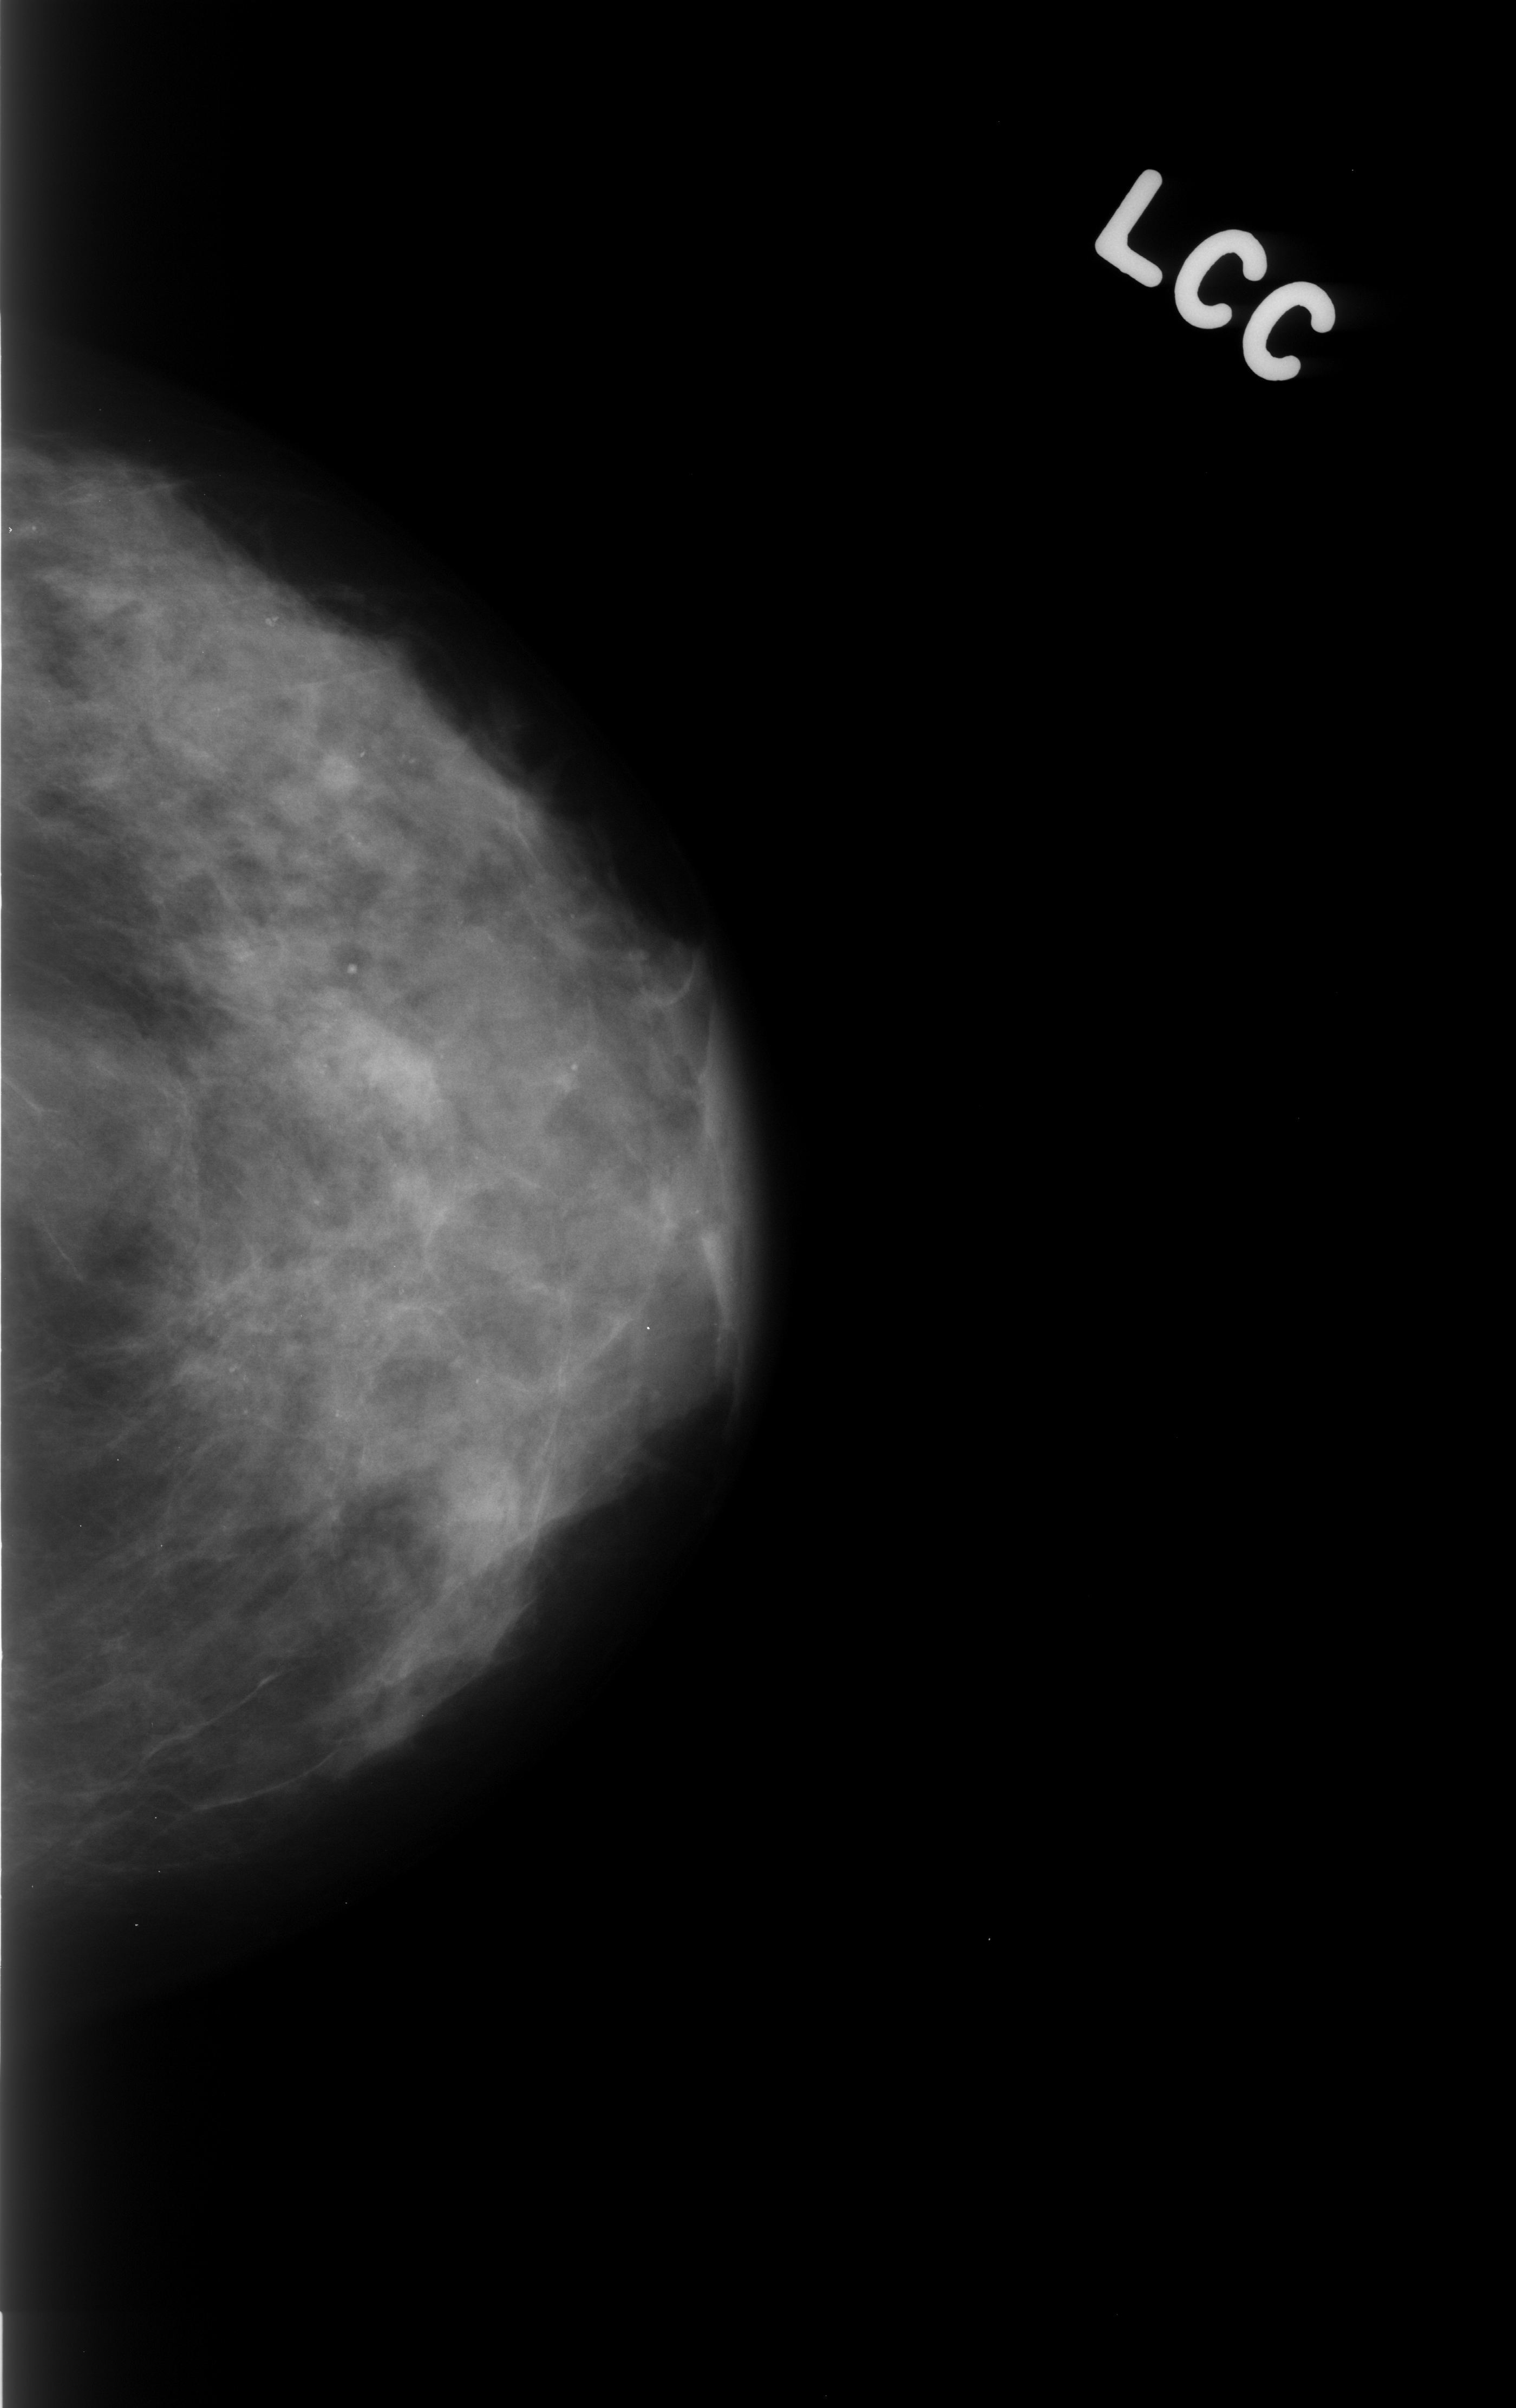
Scanned film-screen mammogram; left breast; craniocaudal (CC) view; breast composition: heterogeneously dense (BI-RADS density category 3 of 4).
Mass, shape round, margins ill defined; BI-RADS assessment category 4; subtlety rating 4 on a 1 (subtle) to 5 (obvious) scale; pathology result (as recorded, not read from the image): benign.